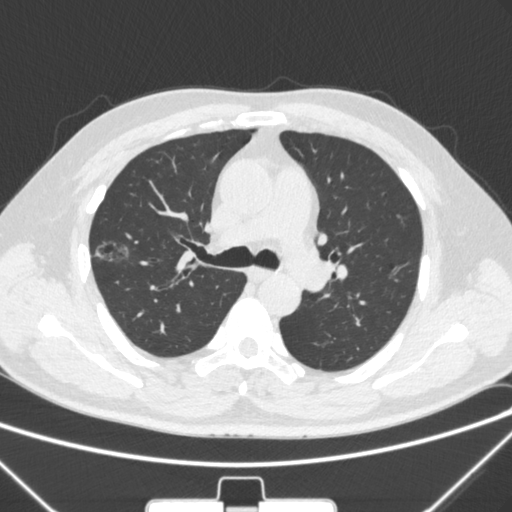
Chest CT, one axial slice. Position 199 of 320 along the scan axis. Lung window (W 1500 / L -600 HU). 1 mm slice thickness. 512 × 512 image matrix, field of view 350 × 350 mm. Patient: male, 58 years. Case-level facts recorded for this patient, not image findings: clinical TNM (as recorded): T1c N0 M0; histopathological grade: G2.
Annotated regions visible in this slice (rectangle marked by the reading radiologist):
- lung tumour (recorded histology: adenocarcinoma): bounding box [x1, y1, x2, y2] px = [83, 233, 137, 284]